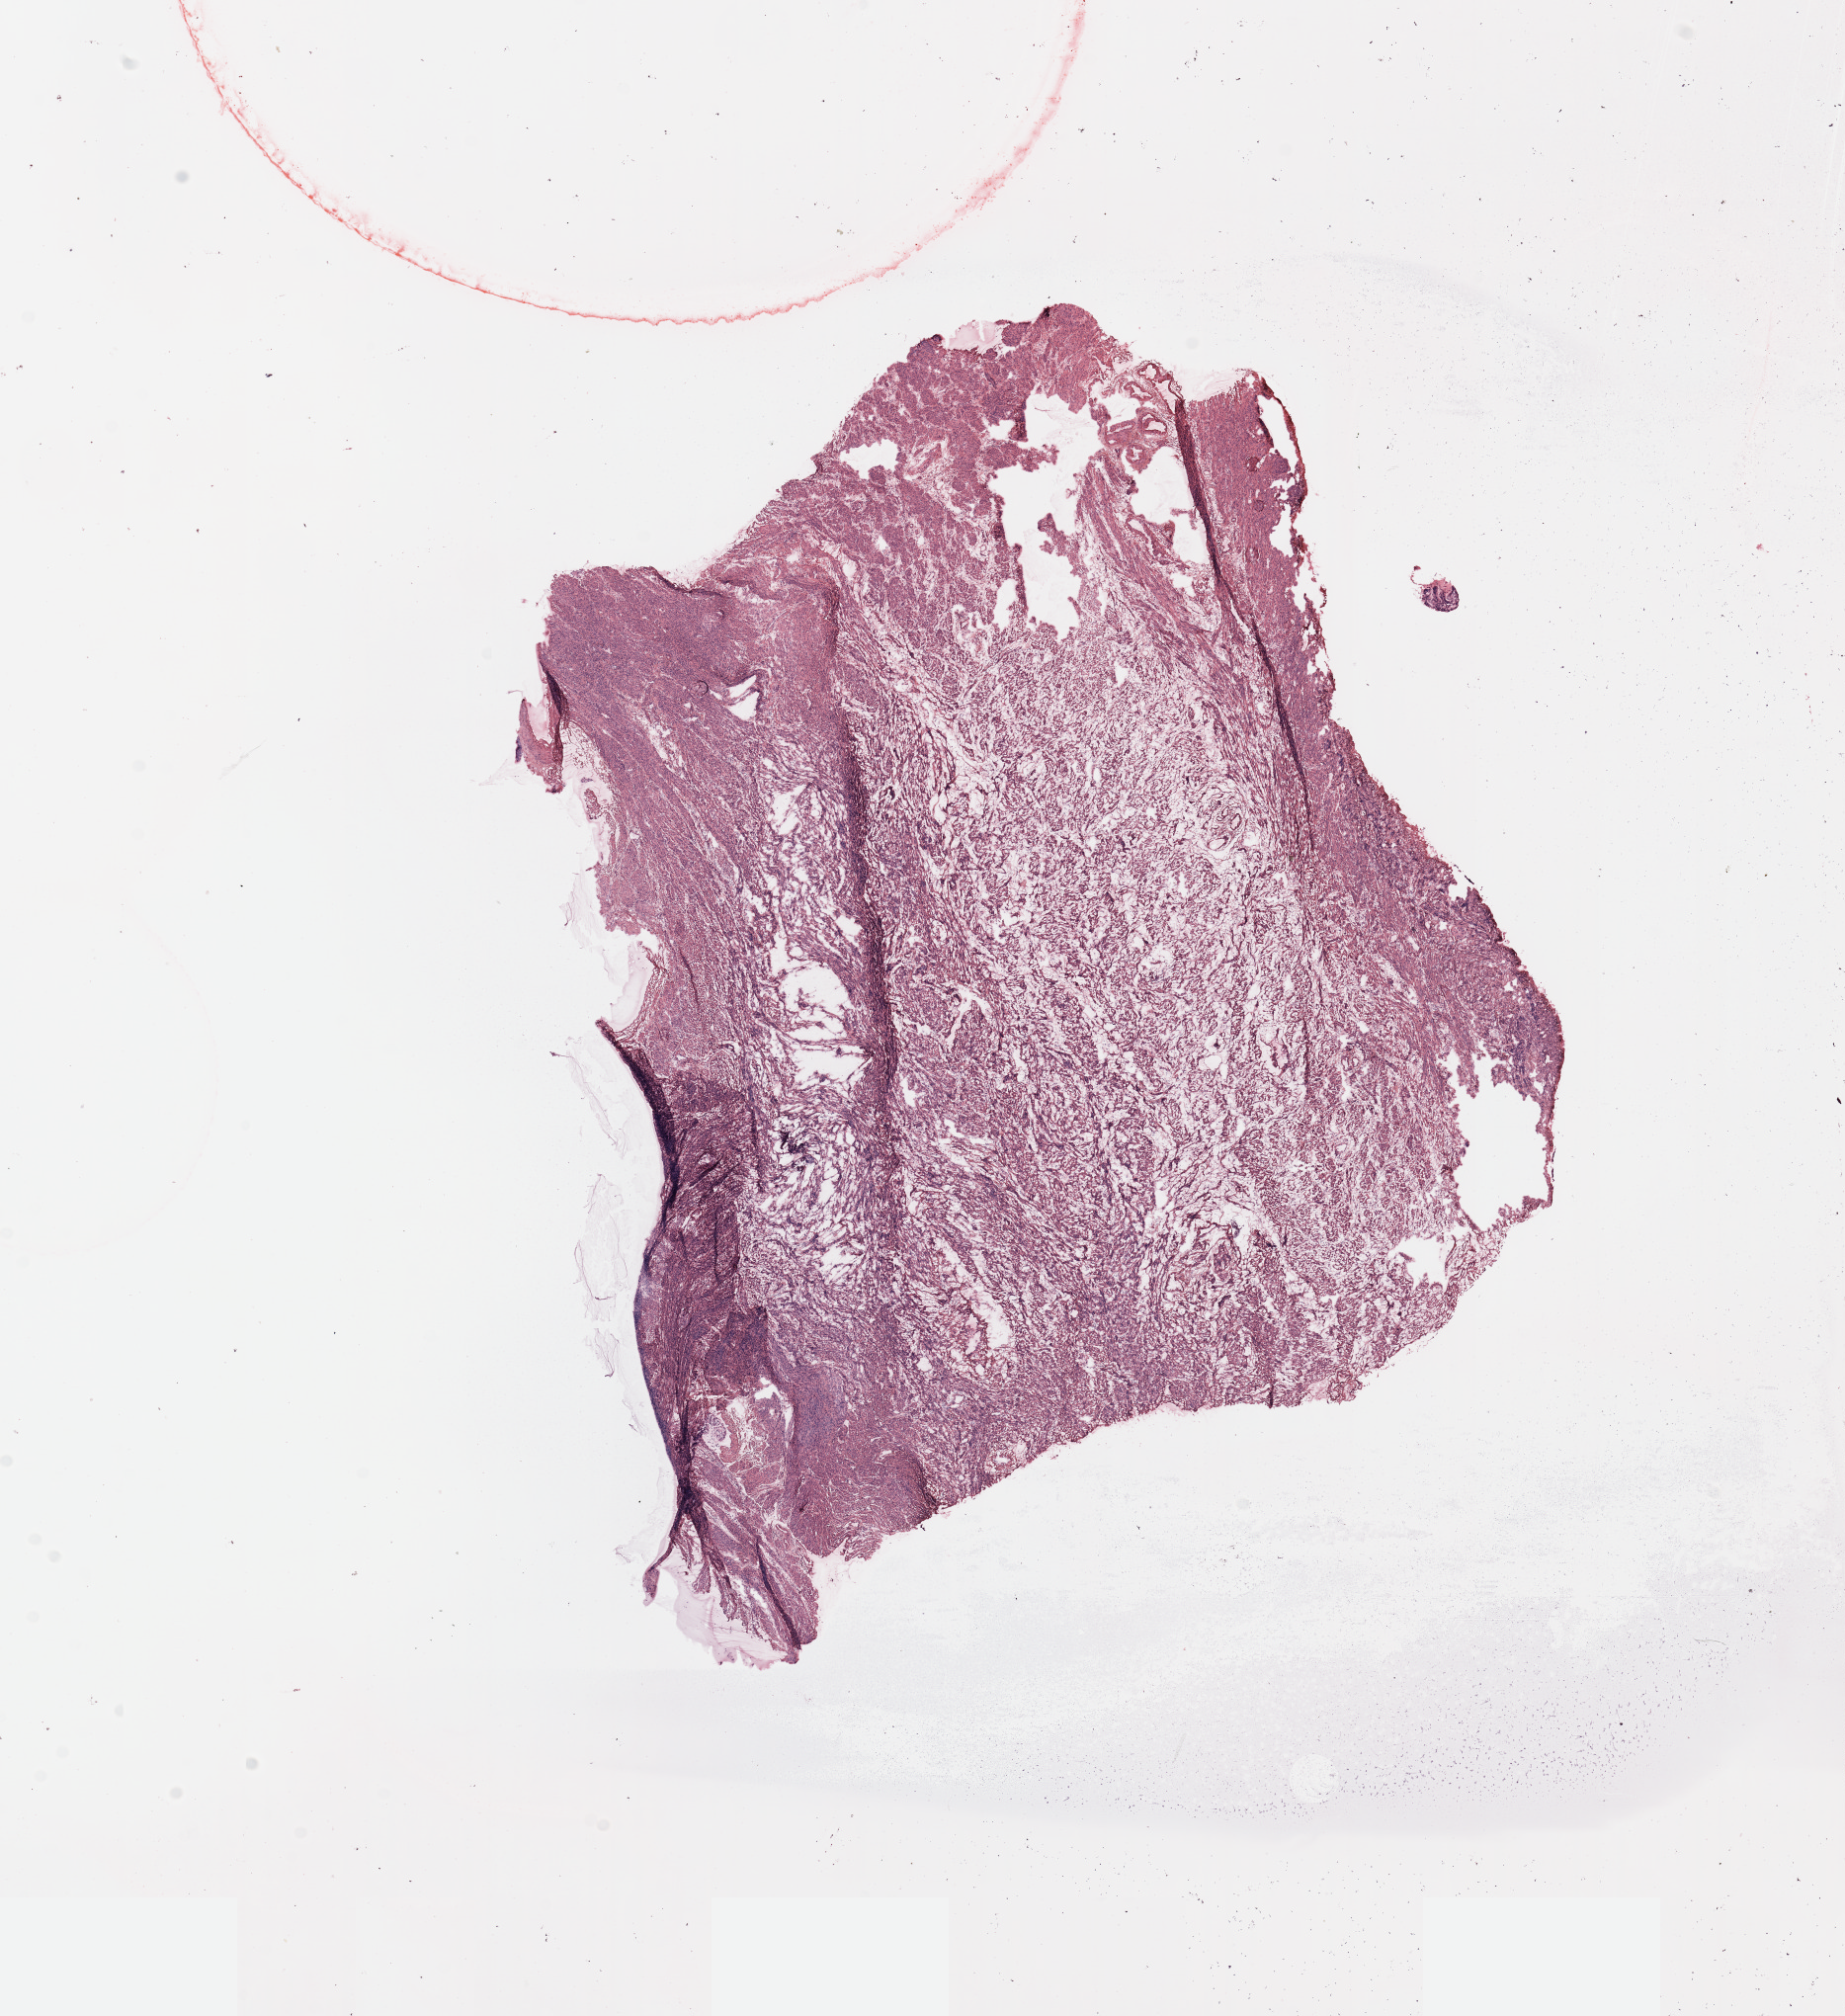
Digitized Hematoxylin and eosin (H&E) stained tissue section (whole slide), shown as a low-resolution overview of the whole scanned area (about 14.8 x 16.1 mm). Normal (non-tumour) tissue sample, uterus. 68-year-old female patient.
* this section: normal (non-tumour) tissue from the same patient
* patient diagnosis: Endometrioid adenocarcinoma, NOS